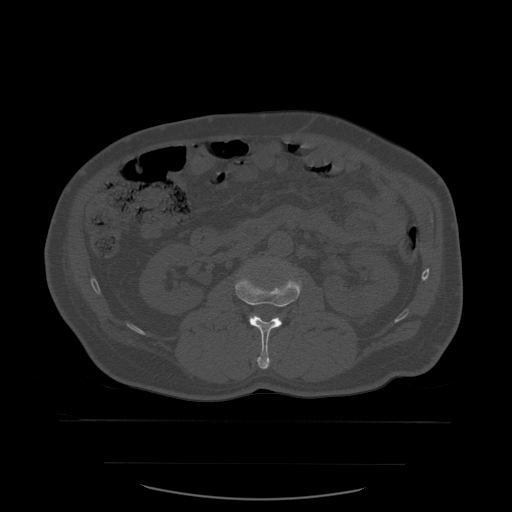
CT including the spine, one axial slice. Position 214 of 590 along the scan axis. Bone window (W 1800 / L 400 HU). 1.25 mm slice thickness. 512 × 512 image matrix, field of view 479 × 479 mm. Patient age 71 years. Case-level facts recorded for this patient, not image findings: primary cancer: lung; vertebrae with lytic lesions (as recorded): T1, T2, L5, S1.
Outlined on this slice (semi-automatic segmentation, software-assisted and operator-edited):
- L2 vertebra: bounding box [x1, y1, x2, y2] px = [235, 274, 302, 370]